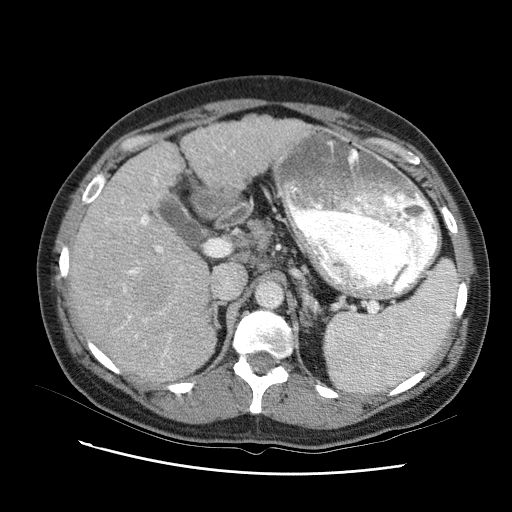
Contrast-enhanced abdominal CT (liver protocol), one axial slice; slice 58 of 95 in the series (ordered by position); reconstruction kernel STANDARD; 120 kVp; one of 2 acquisitions stored at this slice position; soft-tissue window (W 400 / L 40 HU); 2.5 mm slice thickness; 512 × 512 image matrix, field of view 360 × 360 mm. Case-level facts recorded for this patient, not image findings: diagnosis: hepatocellular carcinoma (patient treated with transarterial chemoembolisation; whether this scan precedes or follows treatment is not stated here); TNM stage (as recorded): Stage-I; Child-Pugh class: B; tumour differentiation: moderately differentiated; tumour nodularity: uninodular.
Structures marked on this image (semi-automatically segmented with operator editing):
- liver parenchyma outside the tumour (the mass and vessels are separate outlines, so this box may not span the whole liver): box from (x=68, y=110) to (x=314, y=380) px
- mass: (x=132, y=265)–(x=170, y=305)
- liver vessels: (x=90, y=128)–(x=253, y=341)